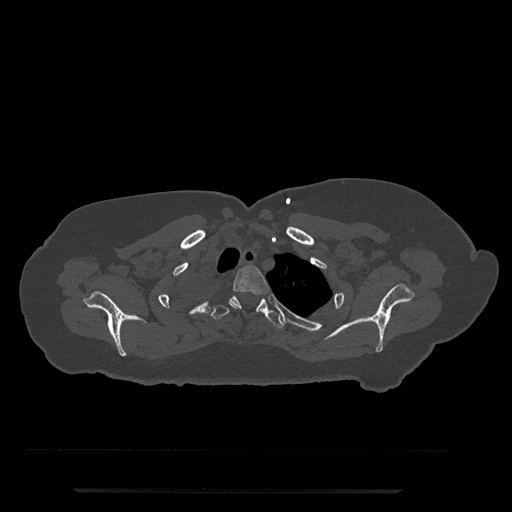
CT including the spine, one axial slice. Reconstruction kernel Br40s/3. Bone window (W 1800 / L 400 HU). 0.5 mm slice thickness. 512 × 512 image matrix, field of view 440 × 440 mm. Female patient, age 51 years. From the clinical record (not read from this slice): primary cancer: neuro; vertebrae with lytic lesions (as recorded): T8.
Annotated regions visible in this slice (semi-automatically segmented with operator editing):
- T2 vertebra: box from (x=229, y=266) to (x=269, y=309) px
- T3 vertebra: (x=210, y=296)–(x=284, y=329)